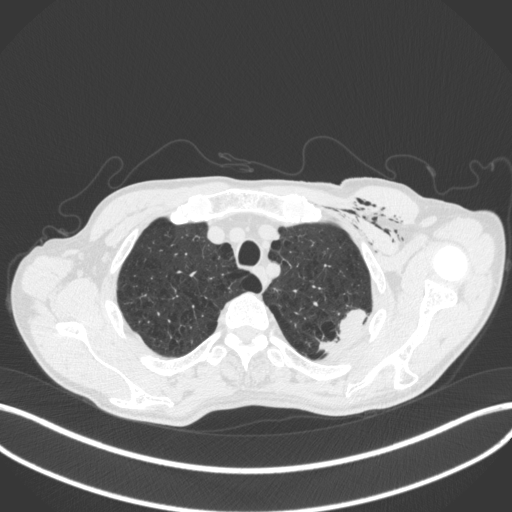
Chest CT, one axial slice. Slice 351 of 416 in the series (ordered by position). Reconstruction kernel B31f. Lung window (W 1500 / L -600 HU). 1 mm slice thickness. 512 × 512 image matrix. Patient: male, 58 years. Case-level facts recorded for this patient, not image findings: clinical TNM (as recorded): T3 N0 M0.
Annotated regions visible in this slice (rectangle marked by the reading radiologist):
- lung tumour (recorded histology: adenocarcinoma): bounding box <313,307,373,357> (left, top, right, bottom; pixels)